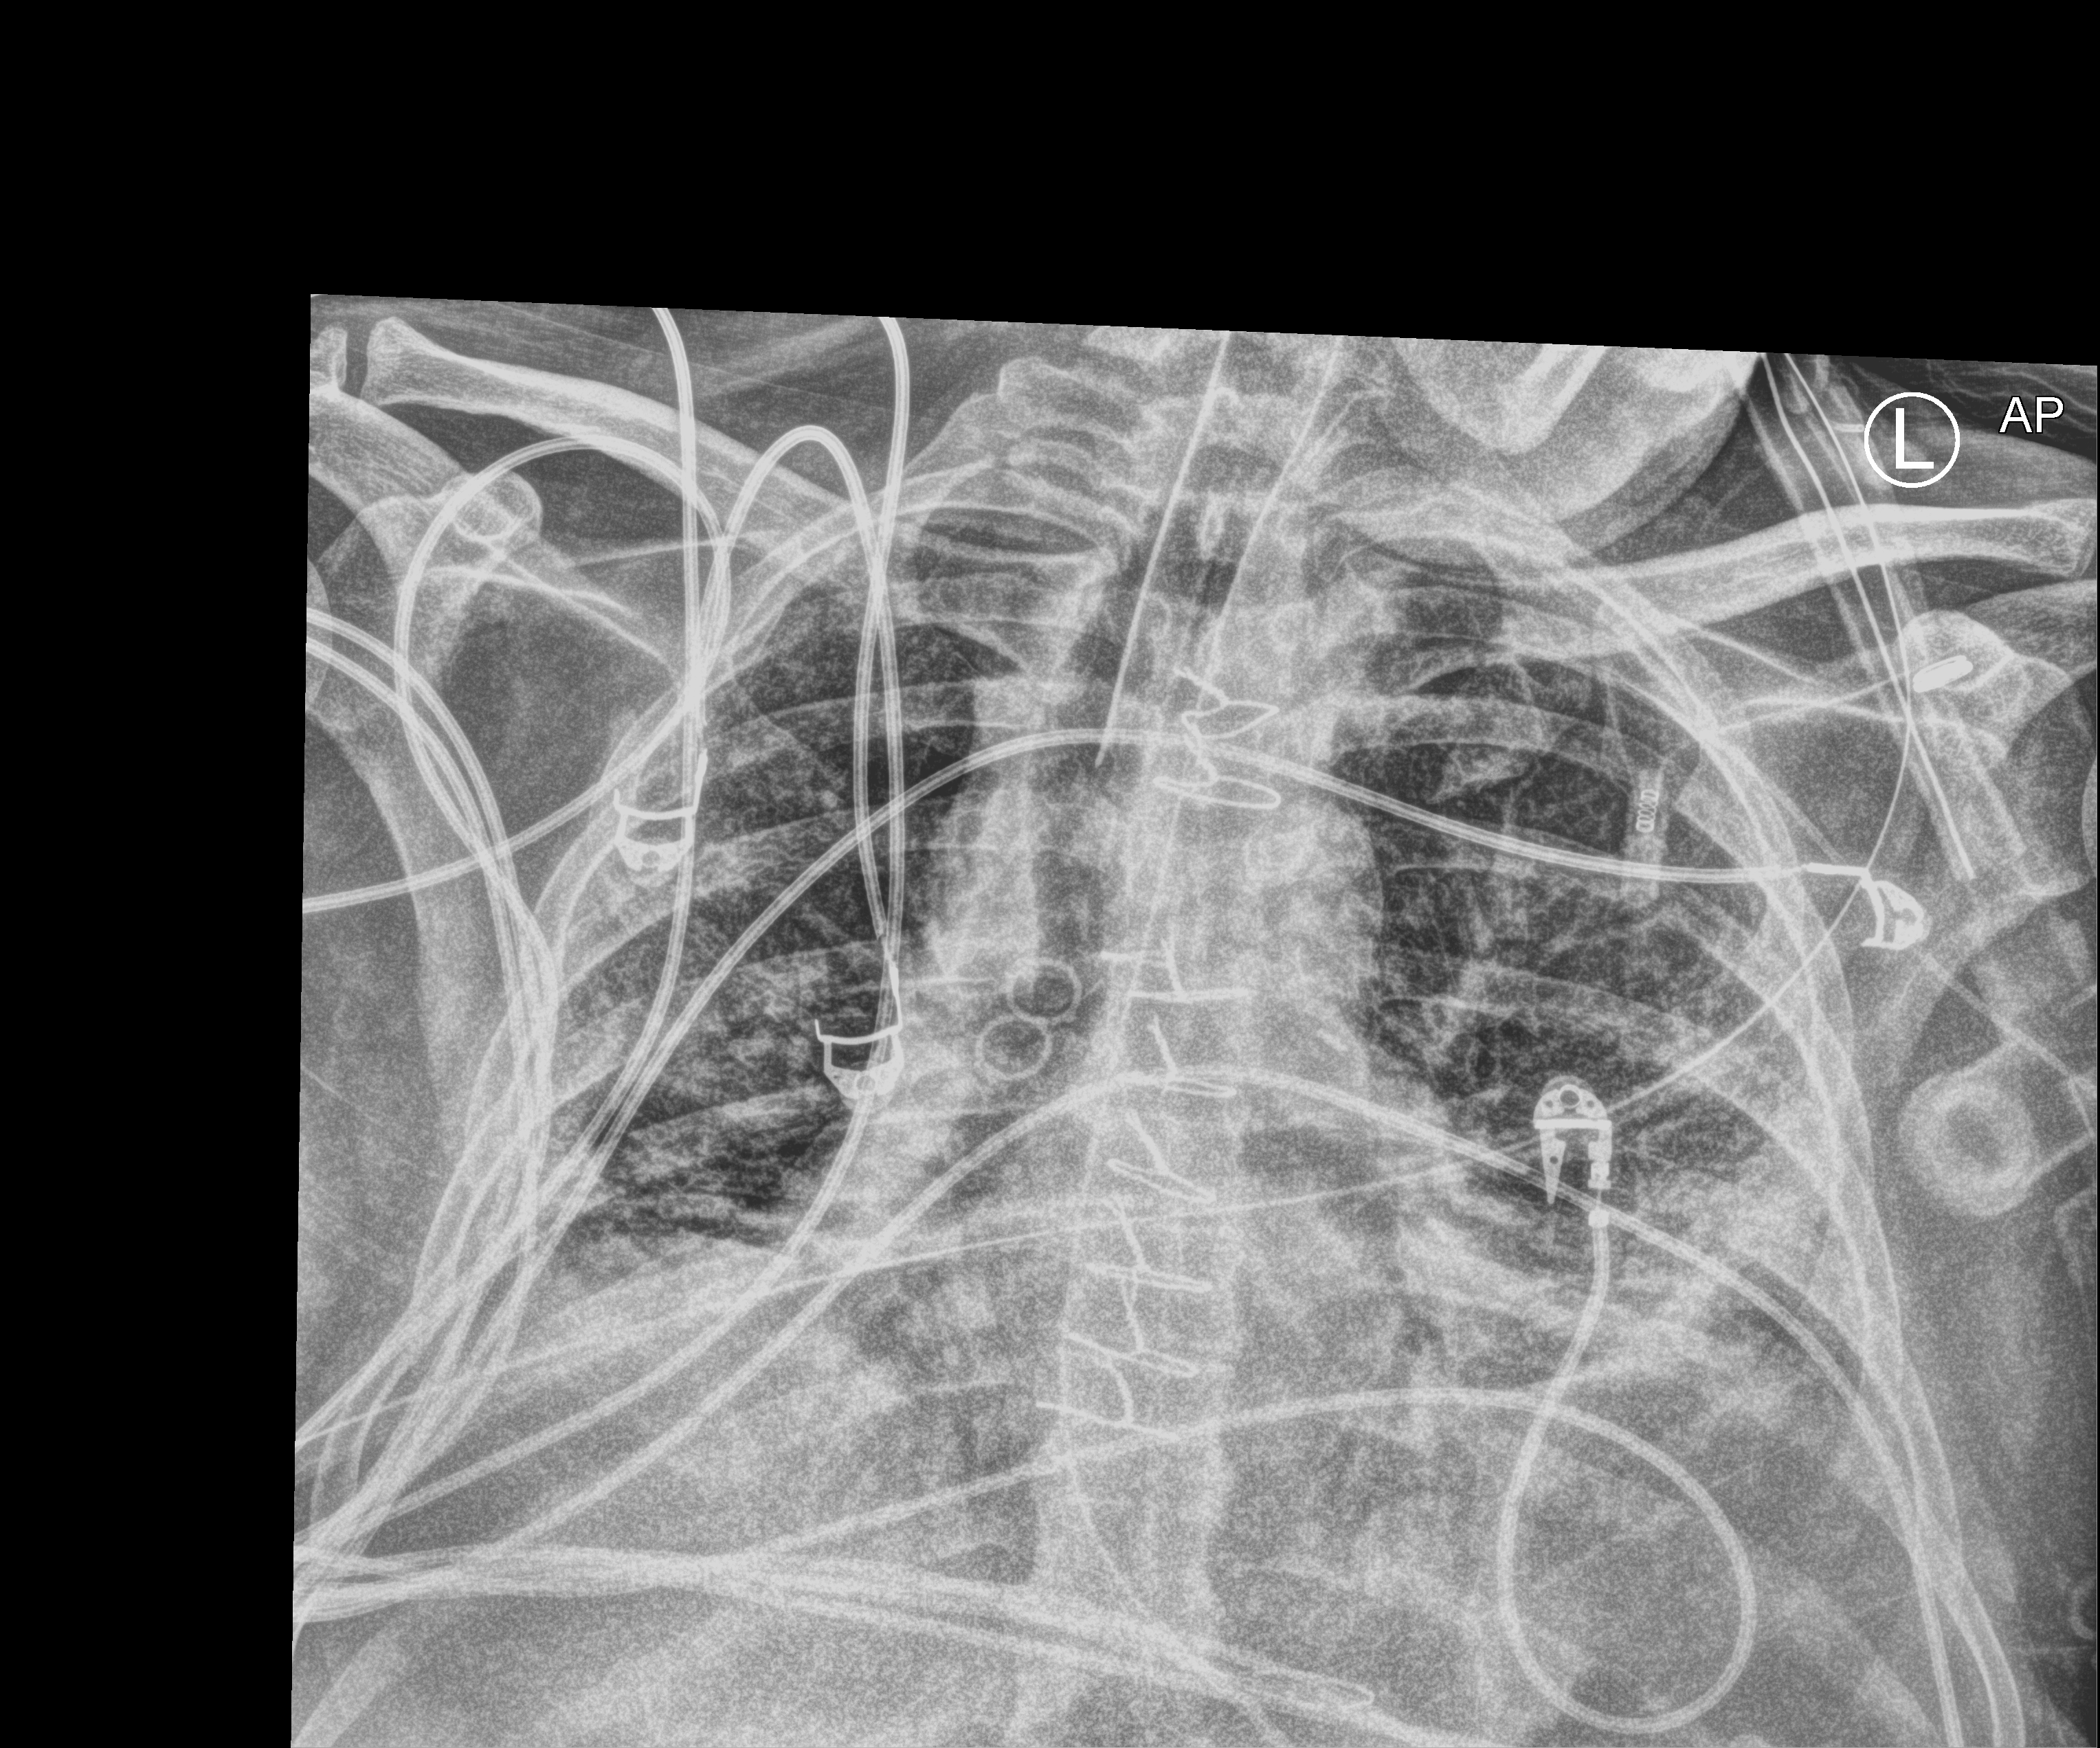
Portable chest radiograph; anteroposterior (AP) projection. Patient hospitalised with COVID-19; male, aged 18–59 years.
Hospital-stay facts (about this admission, not read from this image; timing relative to this image not recorded):
- mechanically ventilated during this hospital stay: yes
- chronic kidney disease (admission record): no